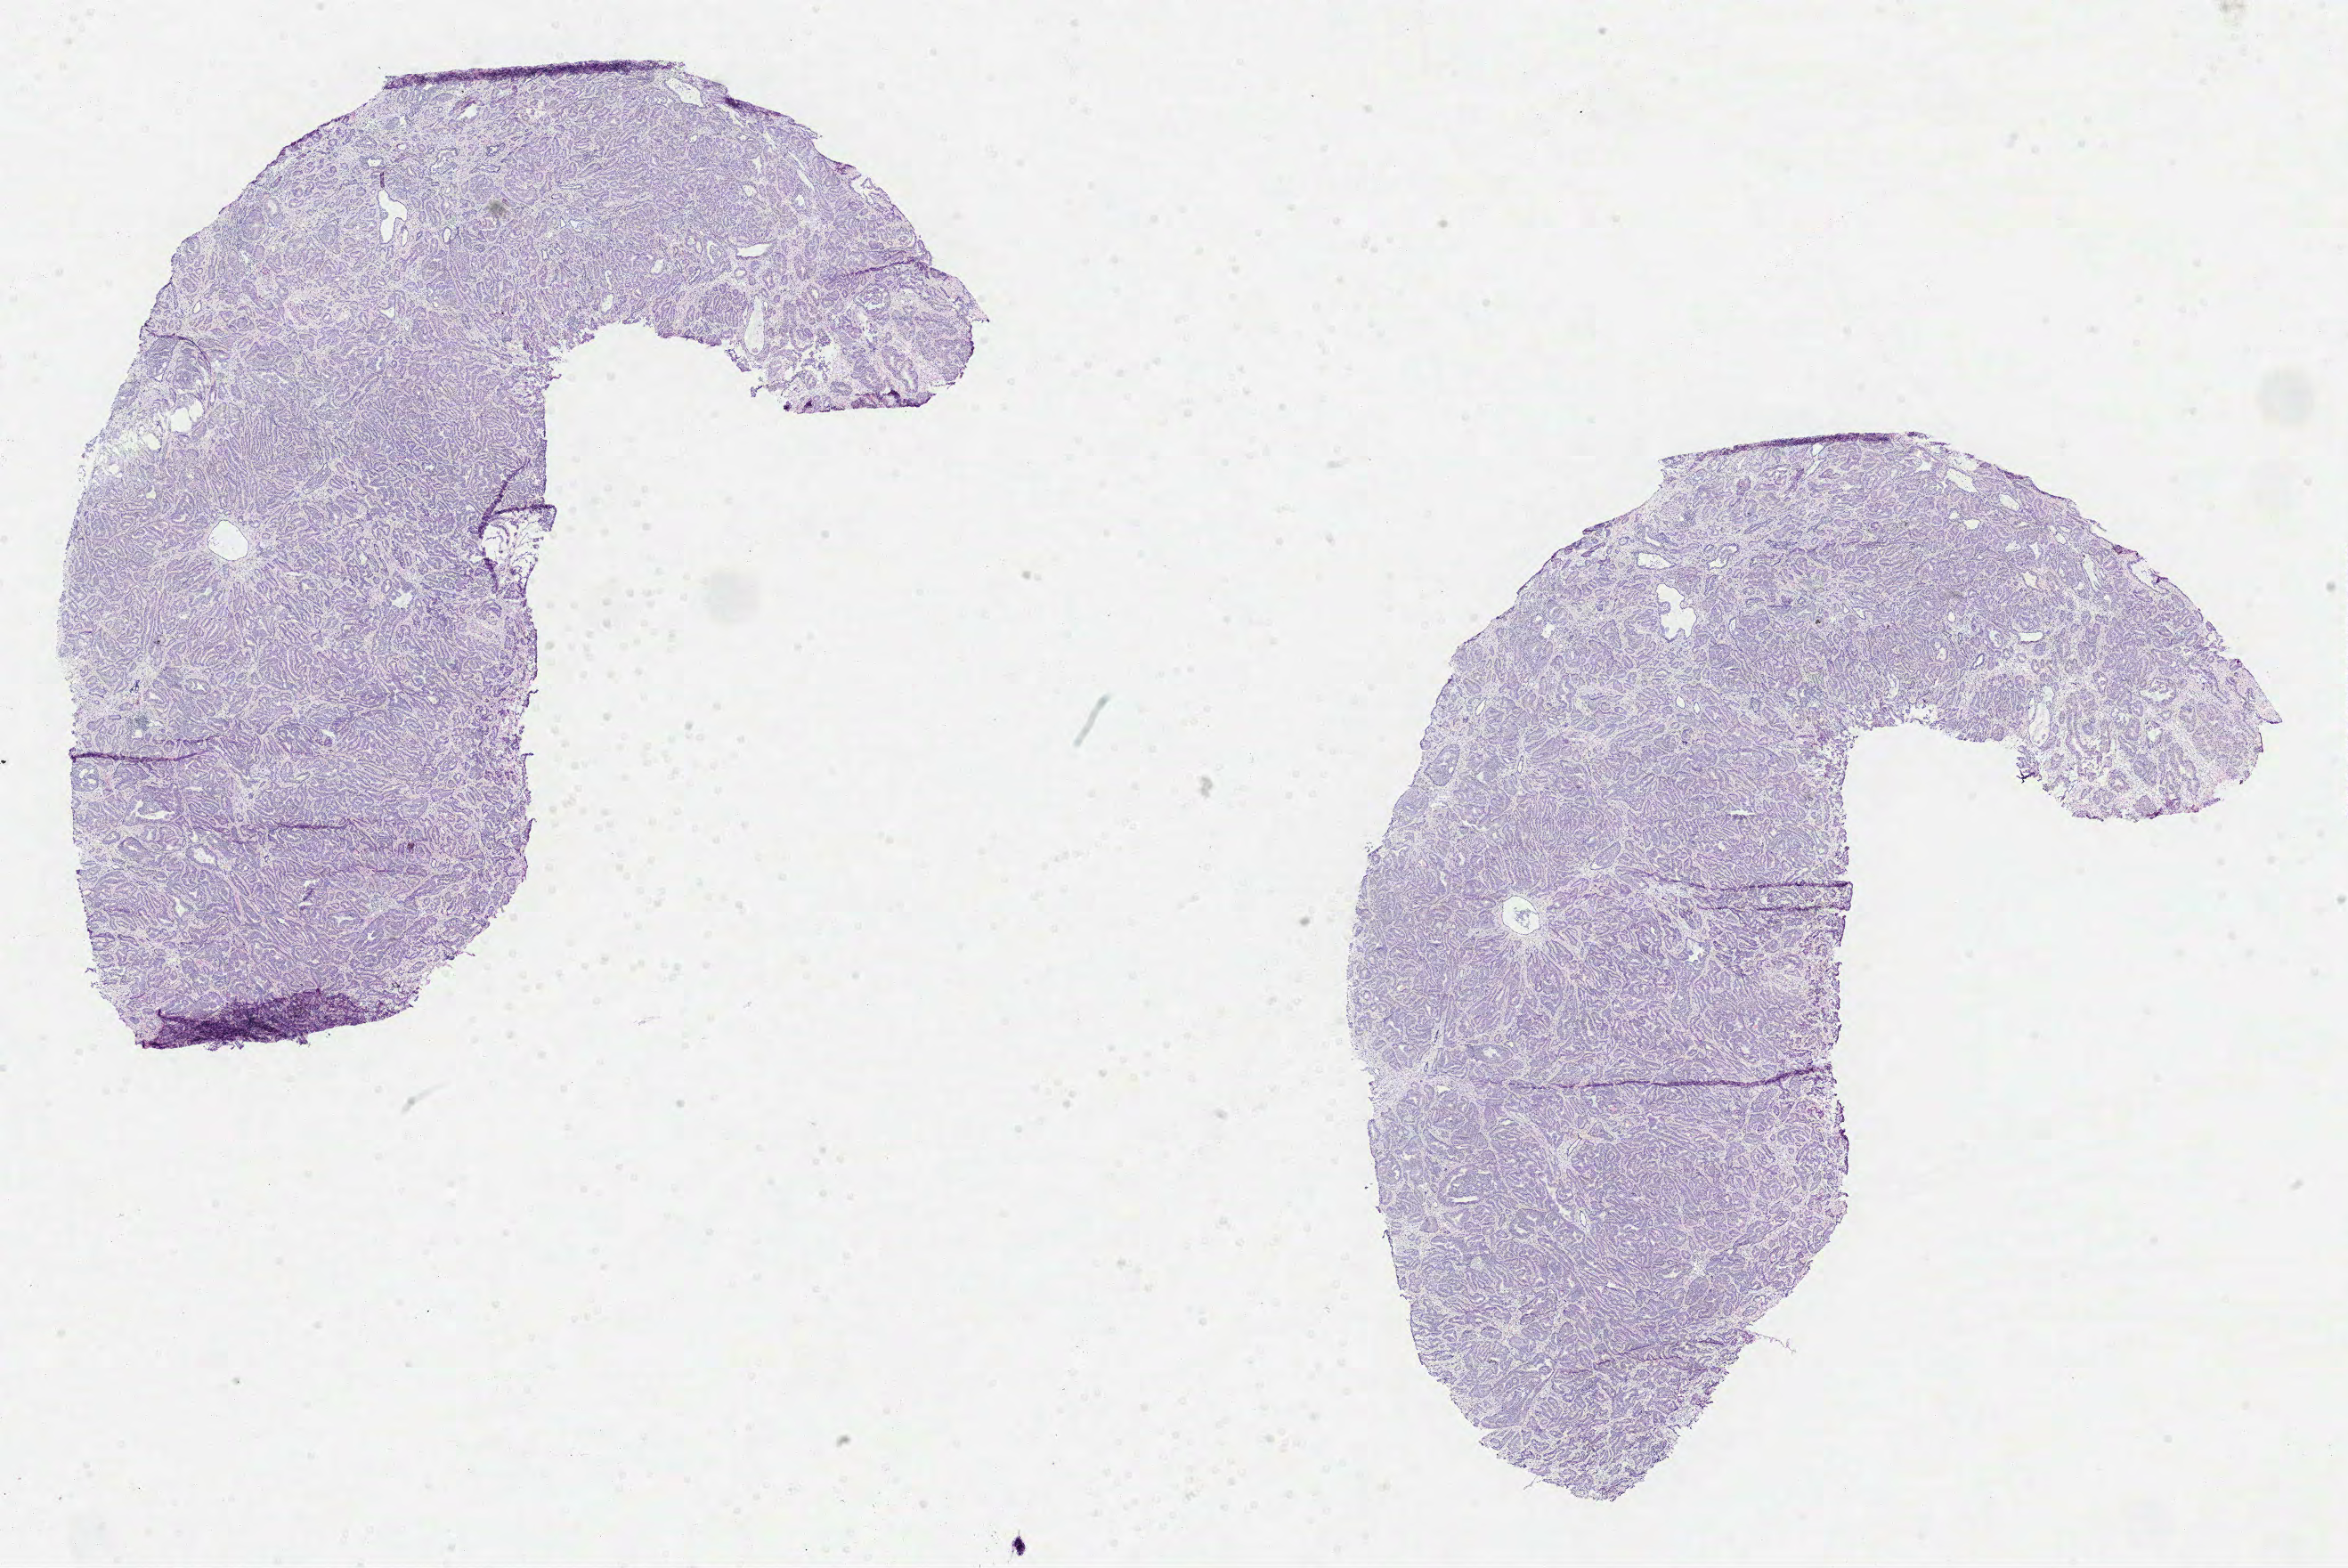
Digitized Hematoxylin and eosin (H&E) stained tissue section (whole slide) — whole scanned area (about 21.3 x 14.2 mm, slide scanned at 40x) shown as a low-resolution overview, formalin-fixed paraffin-embedded (FFPE) diagnostic section, primary tumour sample from the prostate. Male patient; age at initial diagnosis 57 years. Gleason score: 7 (3+4).
Lymph nodes positive (case pathology): 0 of 4 examined. Histologic diagnosis: Acinar cell carcinoma (prostate gland).